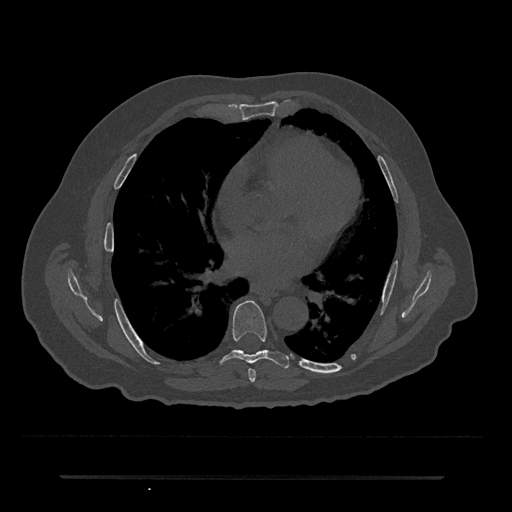
CT including the spine, one axial slice; position 388 of 797 along the scan axis; bone window (W 1800 / L 400 HU); 0.5 mm slice thickness; 512 × 512 image matrix. Patient: male, 69 years. Case-level facts recorded for this patient, not image findings: primary cancer: prostate.
Annotated regions visible in this slice (semi-automatically segmented with operator editing):
- T6 vertebra: bounding box (x1, y1, x2, y2) in pixels: (249, 368, 256, 382)
- T7 vertebra: (220, 300, 289, 368)